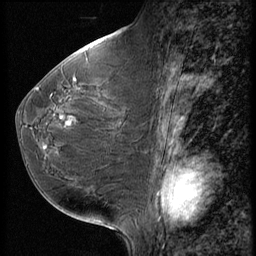
Breast MRI (dynamic contrast-enhanced), one sagittal slice; position 27 of 56 along the scan axis; 3 images stored at this slice position (order not interpretable as contrast timing); 1.5 T; TE 4.2 ms, TR 9 ms; 2.5 mm slice thickness; 256 × 256 image matrix, field of view 180 × 180 mm. Patient: female, 49 years. From the clinical record (not read from this slice): setting: breast cancer imaged before/during neoadjuvant chemotherapy; receptor status: HER2-positive.
Structures marked on this image (semi-automatically segmented with operator editing):
- analysis volume of interest (the breast-tissue region the enhancement analysis was run in; not a lesion): bounding box (x1, y1, x2, y2) in pixels: (17, 74, 148, 198)
- tumour enhancement mask (voxels above the 140 % enhancement threshold inside the analysis volume of interest): (38, 89, 77, 124)